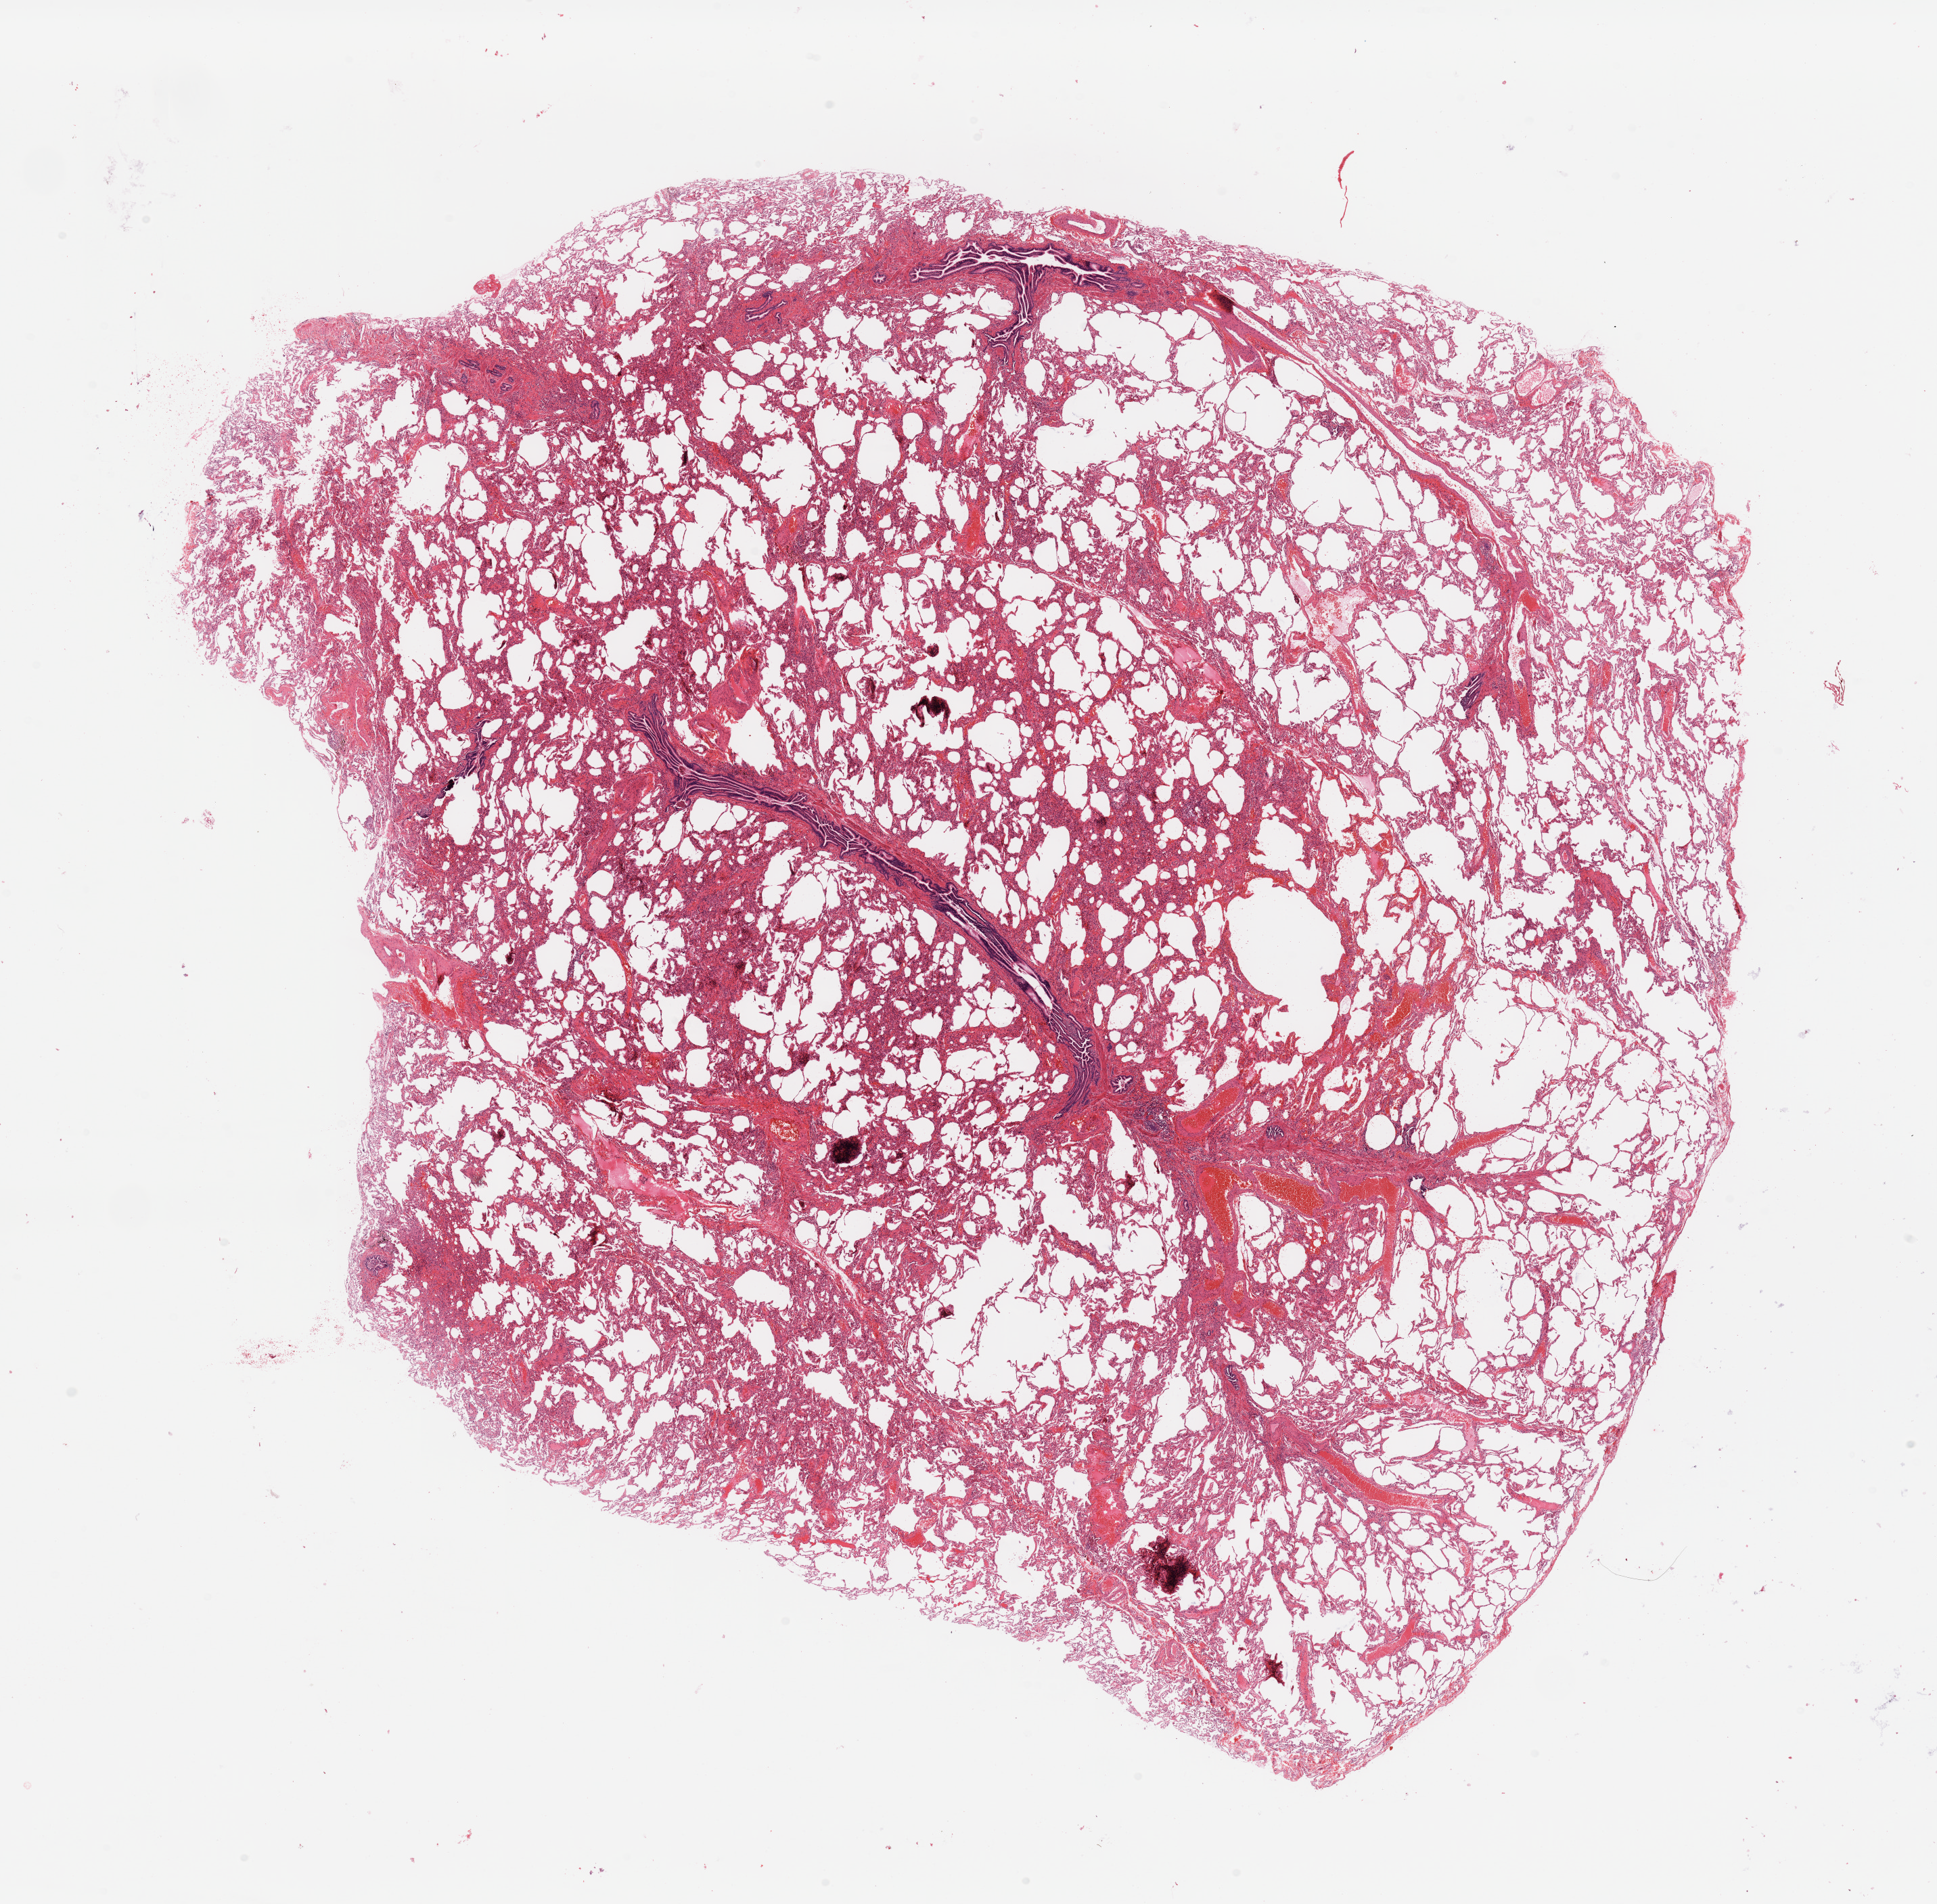
Digitized H&E-stained tissue section (whole slide), a low-resolution overview of the entire scanned area, about 22.6 x 22.3 mm (from a 20x scan), normal (non-tumour) tissue sample, sampled site: lung. Patient: female, age 46 years.
This section: normal (non-tumour) tissue from the same patient. Patient diagnosis: Adenocarcinoma, NOS.